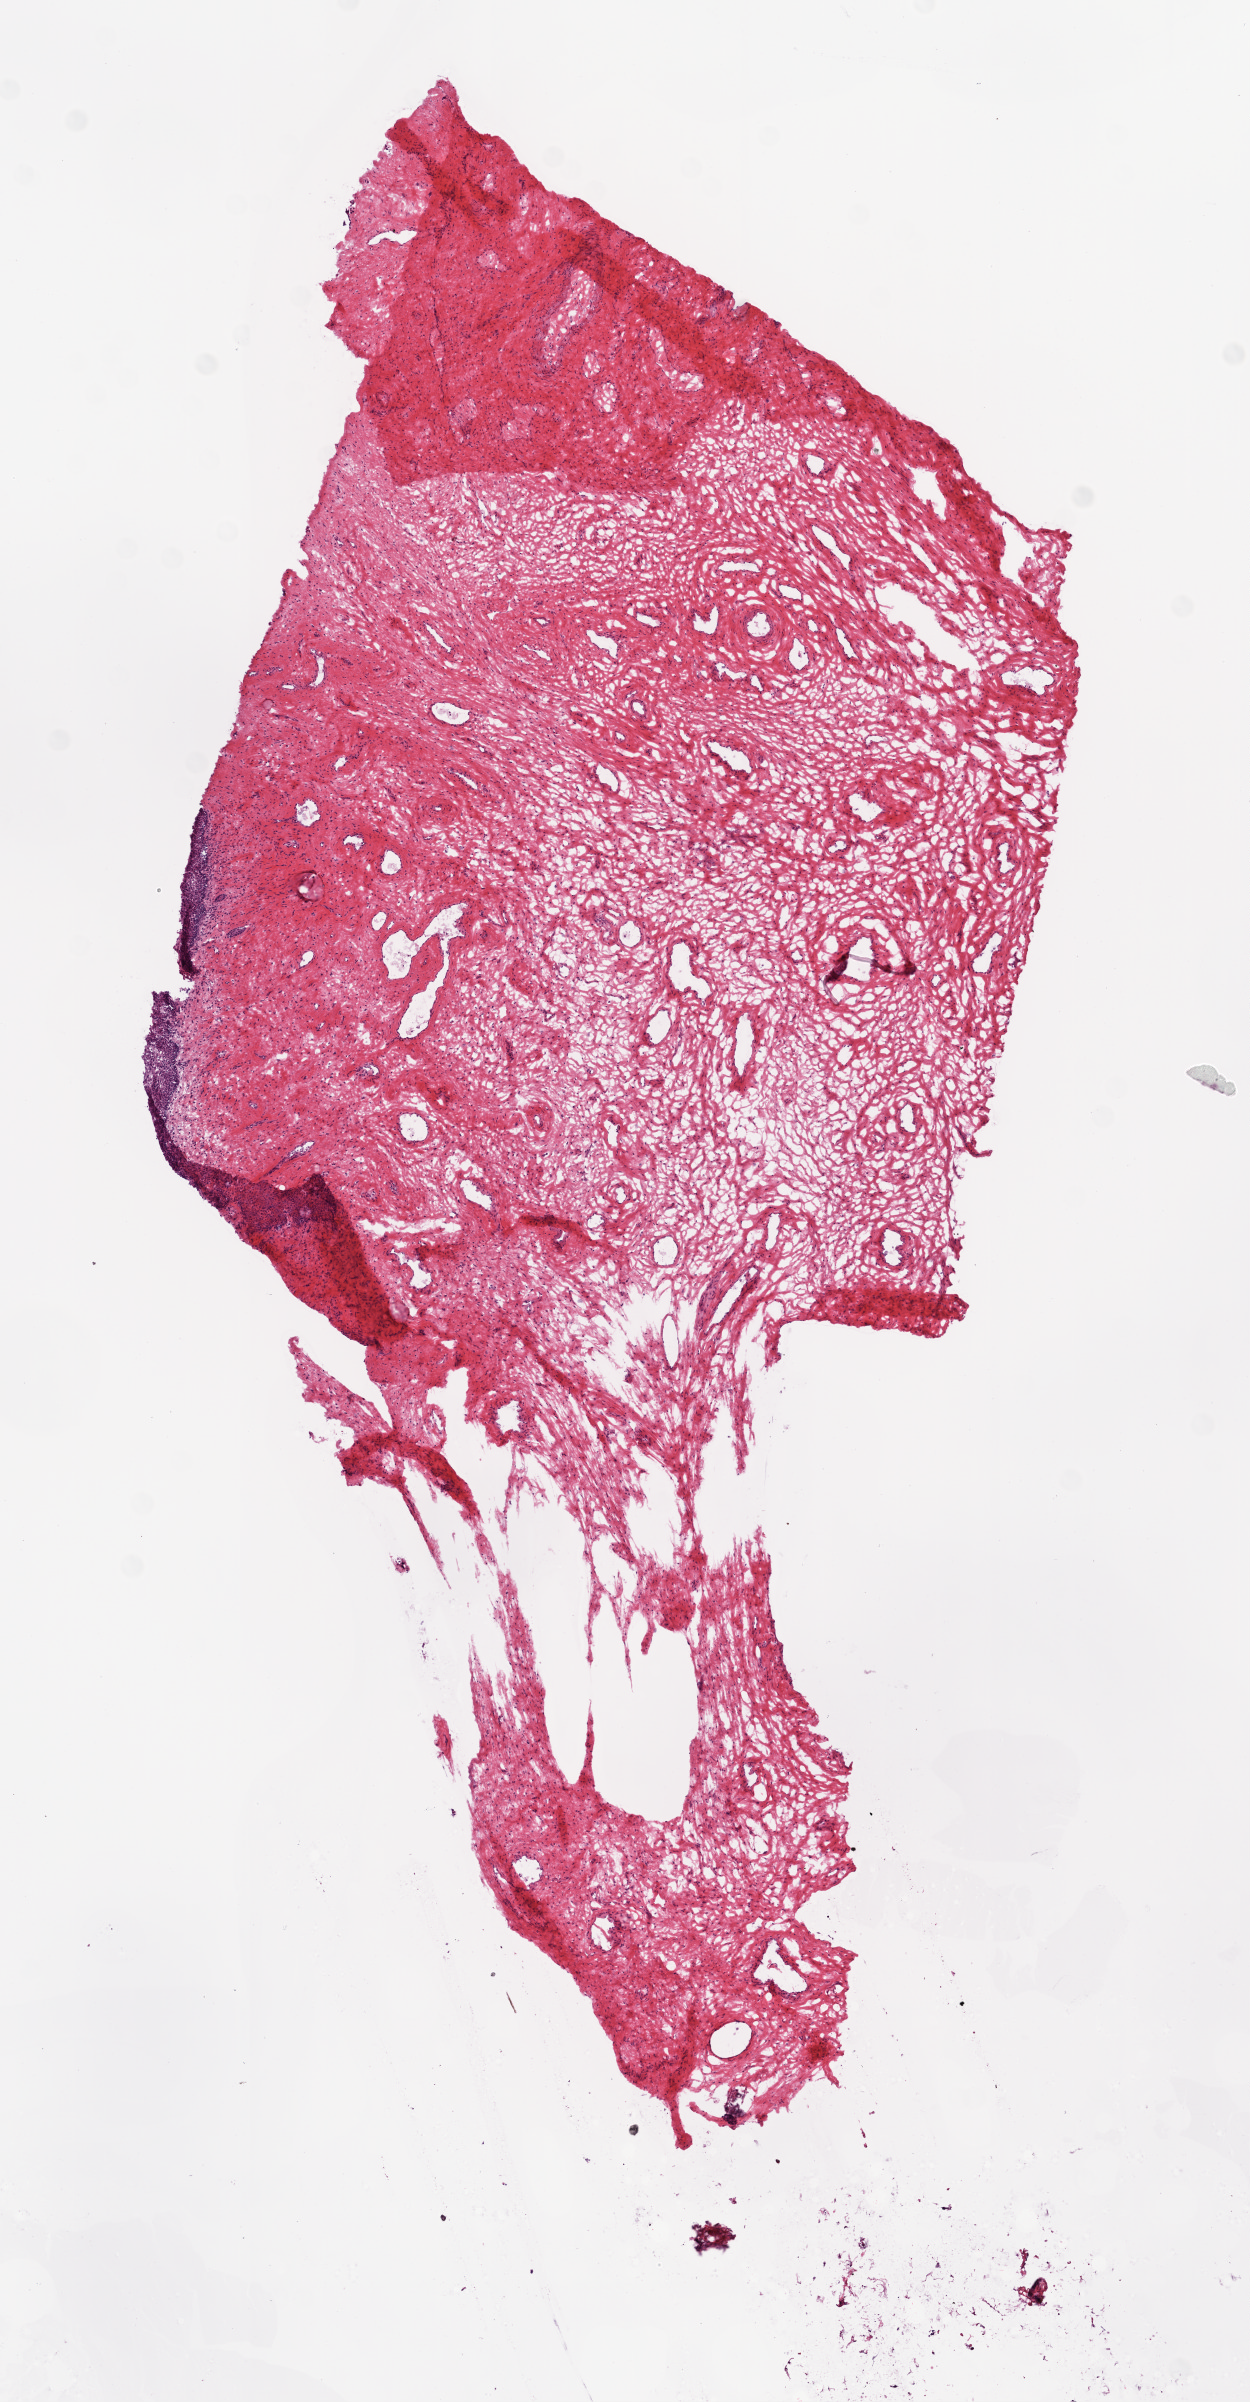
H&E whole-slide image, low-resolution overview of the scanned area, about 5.0 x 9.6 mm; frozen section; solid tissue normal (non-tumour tissue) sample from the ovary. Female patient; age at initial diagnosis 57 years.
- this section: solid tissue normal sample (biorepository sample class)
- patient diagnosis: Serous cystadenocarcinoma, NOS